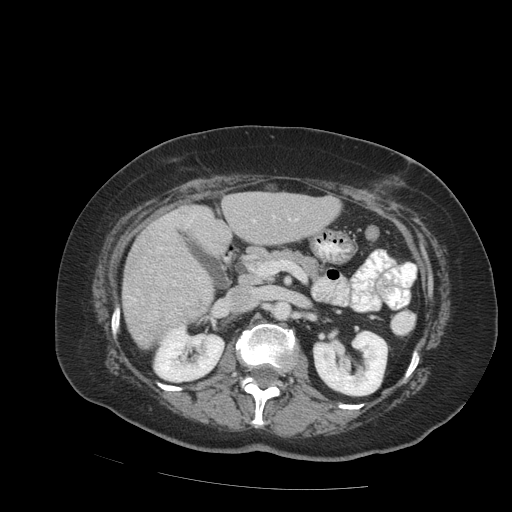
Contrast-enhanced abdominal CT (liver protocol), one axial slice; position 38 of 99 along the scan axis; reconstruction kernel STANDARD; 140 kVp; soft-tissue window (W 400 / L 40 HU); 512 × 512 image matrix, field of view 400 × 400 mm. From the clinical record (not read from this slice): diagnosis: hepatocellular carcinoma (patient treated with transarterial chemoembolisation; whether this scan precedes or follows treatment is not stated here); TNM stage (as recorded): Stage-IVB; Child-Pugh class: A.
Annotated regions visible in this slice (semi-automatically segmented with operator editing):
- liver parenchyma outside the tumour (the mass and vessels are separate outlines, so this box may not span the whole liver): box from (x=122, y=192) to (x=340, y=348) px
- liver vessels: (x=134, y=216)–(x=298, y=300)